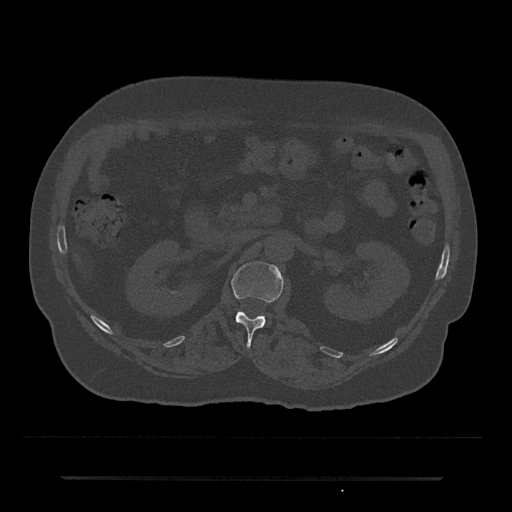
CT including the spine, one axial slice; position 61 of 797 along the scan axis; reconstruction kernel Br40s/3; 120 kVp; bone window (W 1800 / L 400 HU); 512 × 512 image matrix, field of view 437 × 437 mm. Patient: male, 69 years. From the clinical record (not read from this slice): primary cancer: prostate.
Outlined on this slice (semi-automatic segmentation, software-assisted and operator-edited):
- L1 vertebra: box from (x=231, y=261) to (x=283, y=347) px